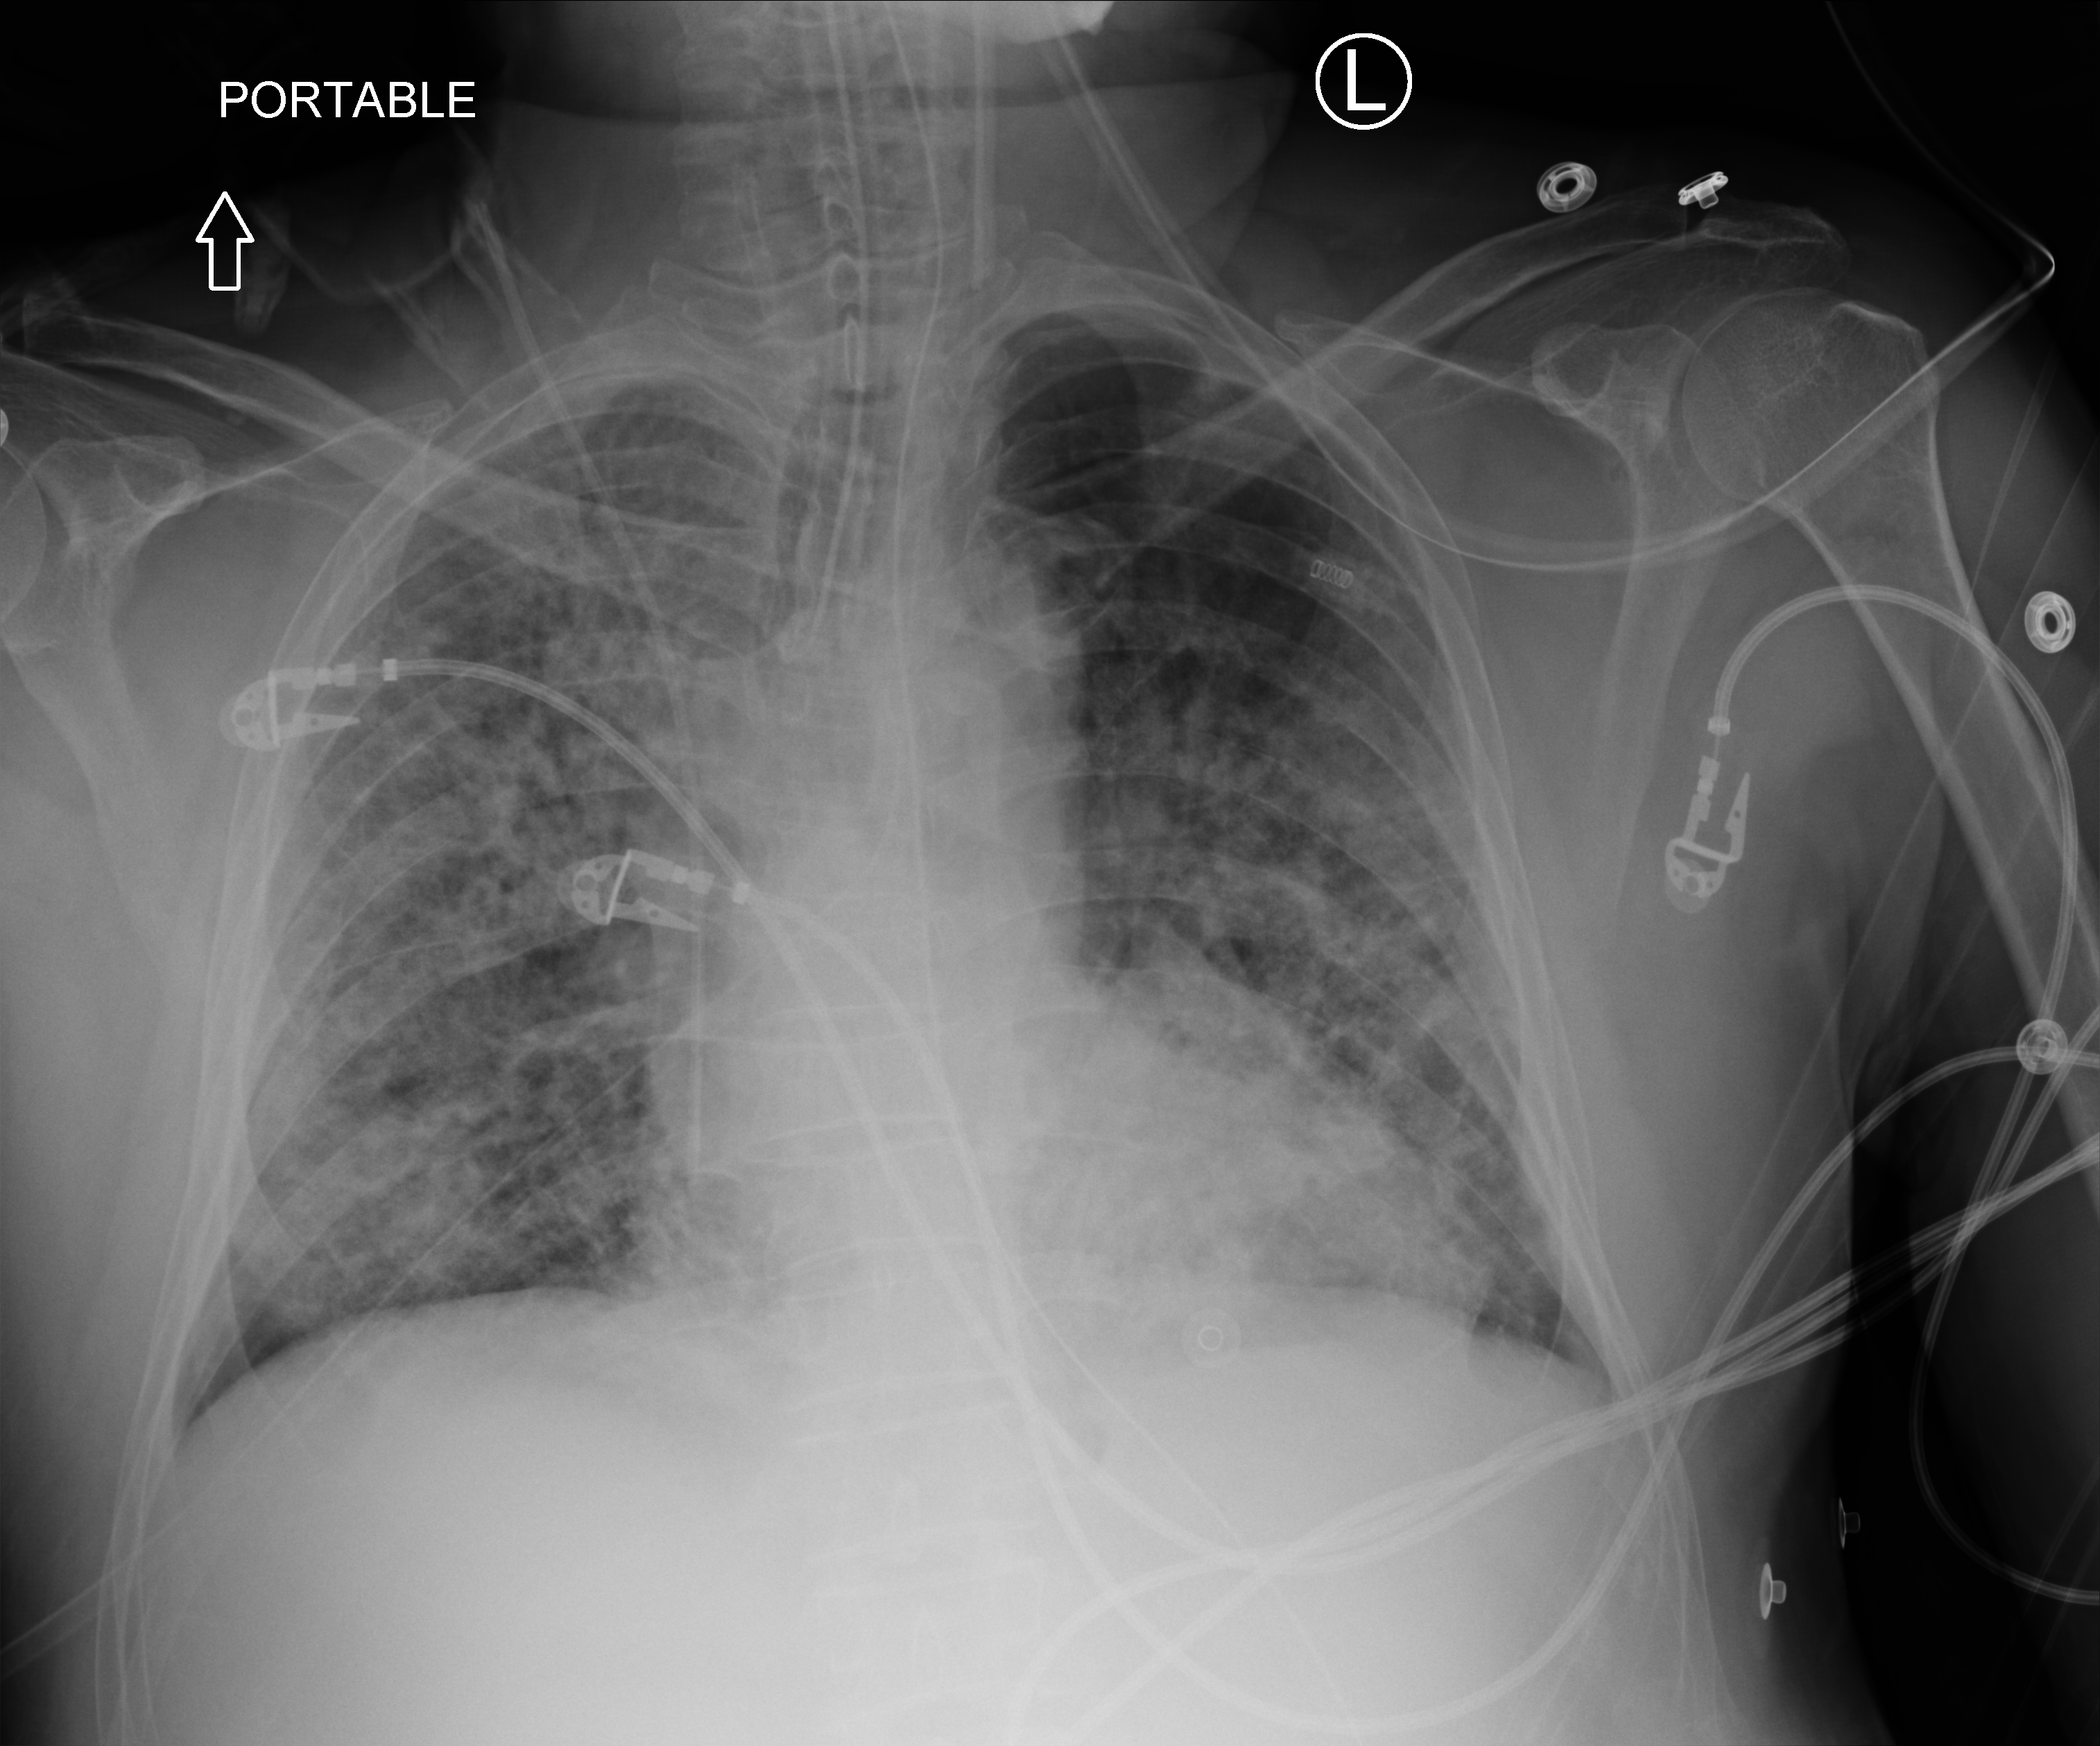
Bedside chest radiograph (computed radiography). Male patient hospitalised with COVID-19, age 60–74 years.
Hospital-stay facts (about this admission, not read from this image; timing relative to this image not recorded):
- mechanically ventilated during this hospital stay: yes
- admitted to intensive care during this hospital stay: yes